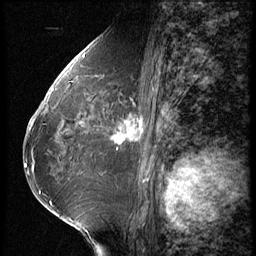
Breast MRI (dynamic contrast-enhanced), one sagittal slice. 3 images stored at this slice position (order not interpretable as contrast timing). 1.5 T. TE 4.2 ms, TR 9 ms. 2.5 mm slice thickness. 256 × 256 image matrix, field of view 180 × 180 mm. Patient: female, 65 years. From the clinical record (not read from this slice): setting: breast cancer imaged before/during neoadjuvant chemotherapy; receptor status: HR-positive, HER2-negative.
Annotated regions visible in this slice (semi-automatic segmentation, software-assisted and operator-edited):
- analysis volume of interest (the breast-tissue region the enhancement analysis was run in; not a lesion): bounding box [x1, y1, x2, y2] px = [104, 104, 154, 161]
- tumour enhancement mask (voxels above the 140 % enhancement threshold inside the analysis volume of interest): [114, 114, 144, 149]